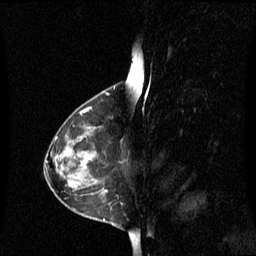
Breast MRI (dynamic contrast-enhanced), one sagittal slice. Position 35 of 60 along the scan axis. Dynamic contrast-enhanced series, image 2 of 3 at this slice position (ordered by acquisition). 1.5 T. TE 4.2 ms, TR 8.4 ms. 256 × 256 image matrix, field of view 240 × 240 mm. Female patient, age 42 years. From the clinical record (not read from this slice): setting: breast cancer imaged before/during neoadjuvant chemotherapy; receptor status: HR-positive, HER2-negative.
Annotated regions visible in this slice (semi-automatic segmentation, software-assisted and operator-edited):
- analysis volume of interest (the breast-tissue region the enhancement analysis was run in; not a lesion): bounding box <60,126,107,195> (left, top, right, bottom; pixels)
- tumour enhancement mask (voxels above the 70 % enhancement threshold inside the analysis volume of interest): <81,156,92,167>